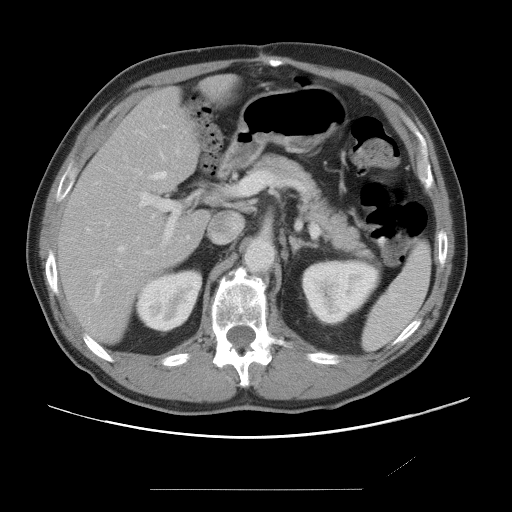
Contrast-enhanced abdominal CT, one axial slice. Slice 41 of 87 in the series (ordered by position). Intravenous contrast given. Soft-tissue window (W 400 / L 40 HU). 5 mm slice thickness. 512 × 512 image matrix, field of view 406 × 406 mm. Male patient, age 74 years. Case-level facts recorded for this patient, not image findings: diagnosis: colorectal cancer liver metastases, imaged before liver resection; multiple liver metastases: yes; largest metastasis: 1.1 cm; chemotherapy before resection: yes.
Annotated regions visible in this slice (outlined manually by an expert reader):
- hepatic veins: box from (x=95, y=135) to (x=179, y=296) px
- liver: (x=59, y=78)–(x=233, y=343)
- planned liver remnant (the part of the liver to remain after resection): (x=59, y=78)–(x=235, y=343)
- portal vein (with intrahepatic branches): (x=139, y=171)–(x=274, y=255)